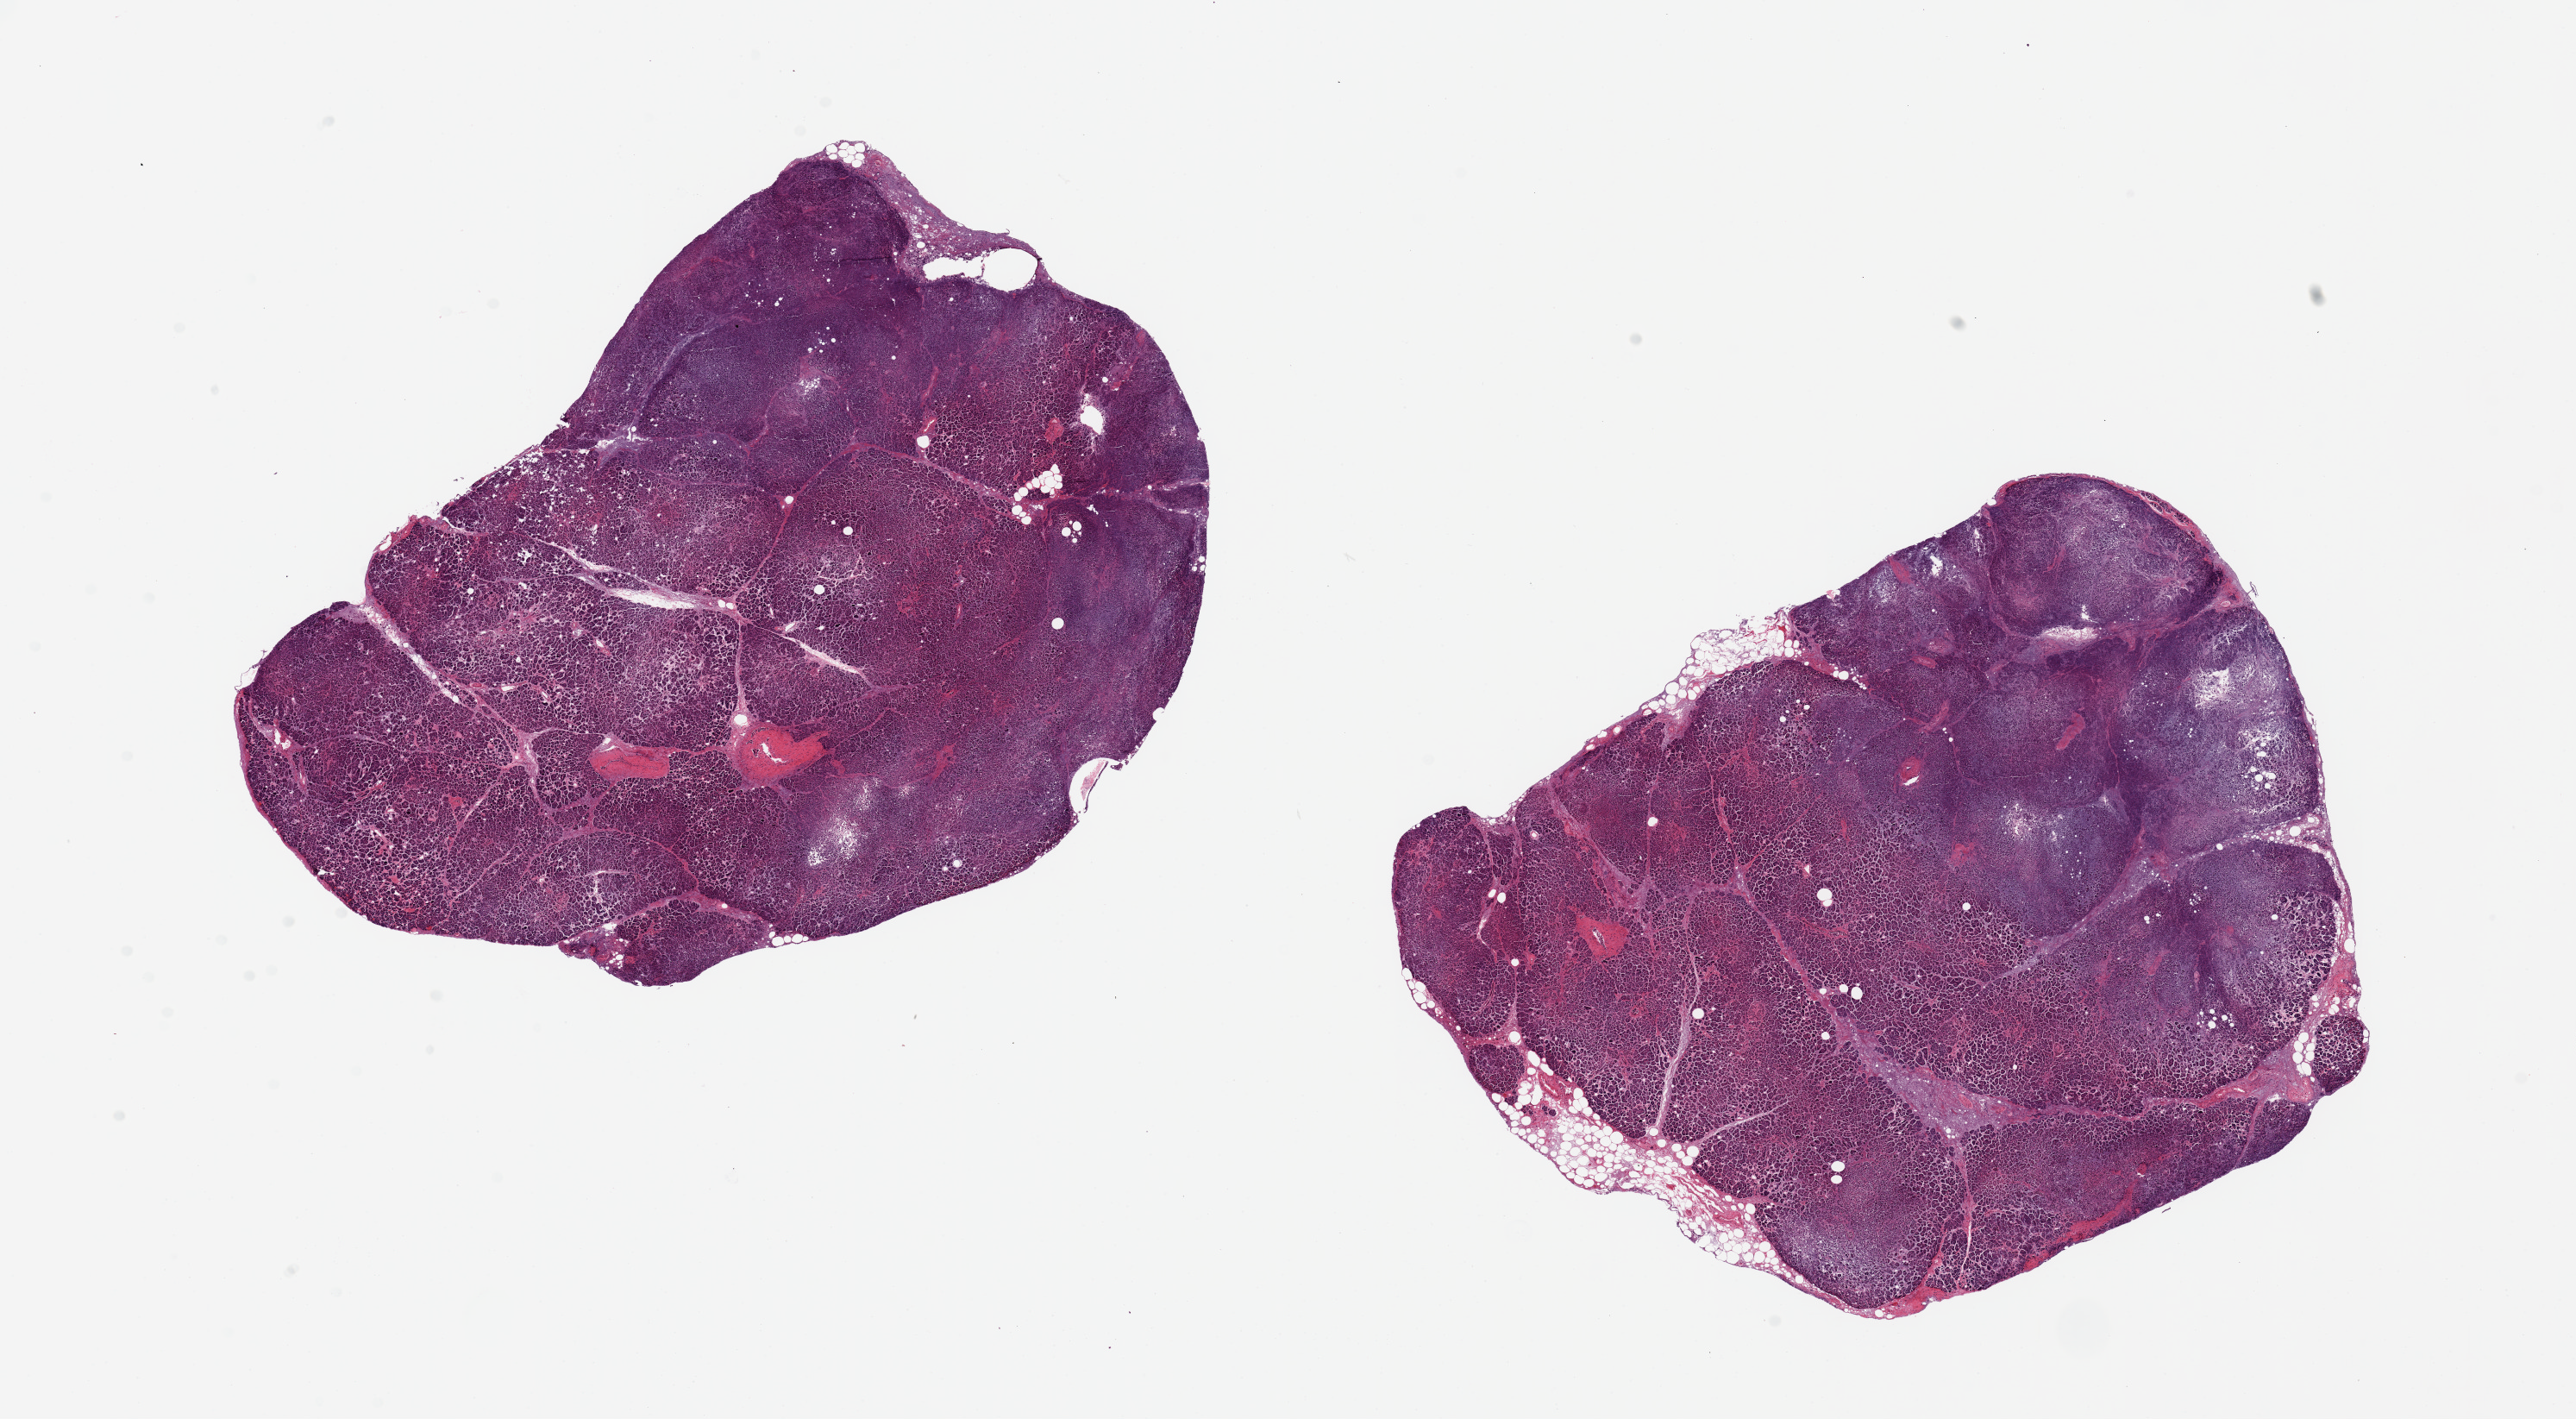
H&E whole-slide image — low-resolution overview of the scanned area, about 23.6 x 13.0 mm, PAXgene-fixed paraffin-embedded (PFPE) section, target tissue: pancreas, donor tissue sample. Donor: male.
Pathologist's review note for this sample: 2 pieces ~8x6mm. Badly autolyzed/saponified. Islets not well visualized.